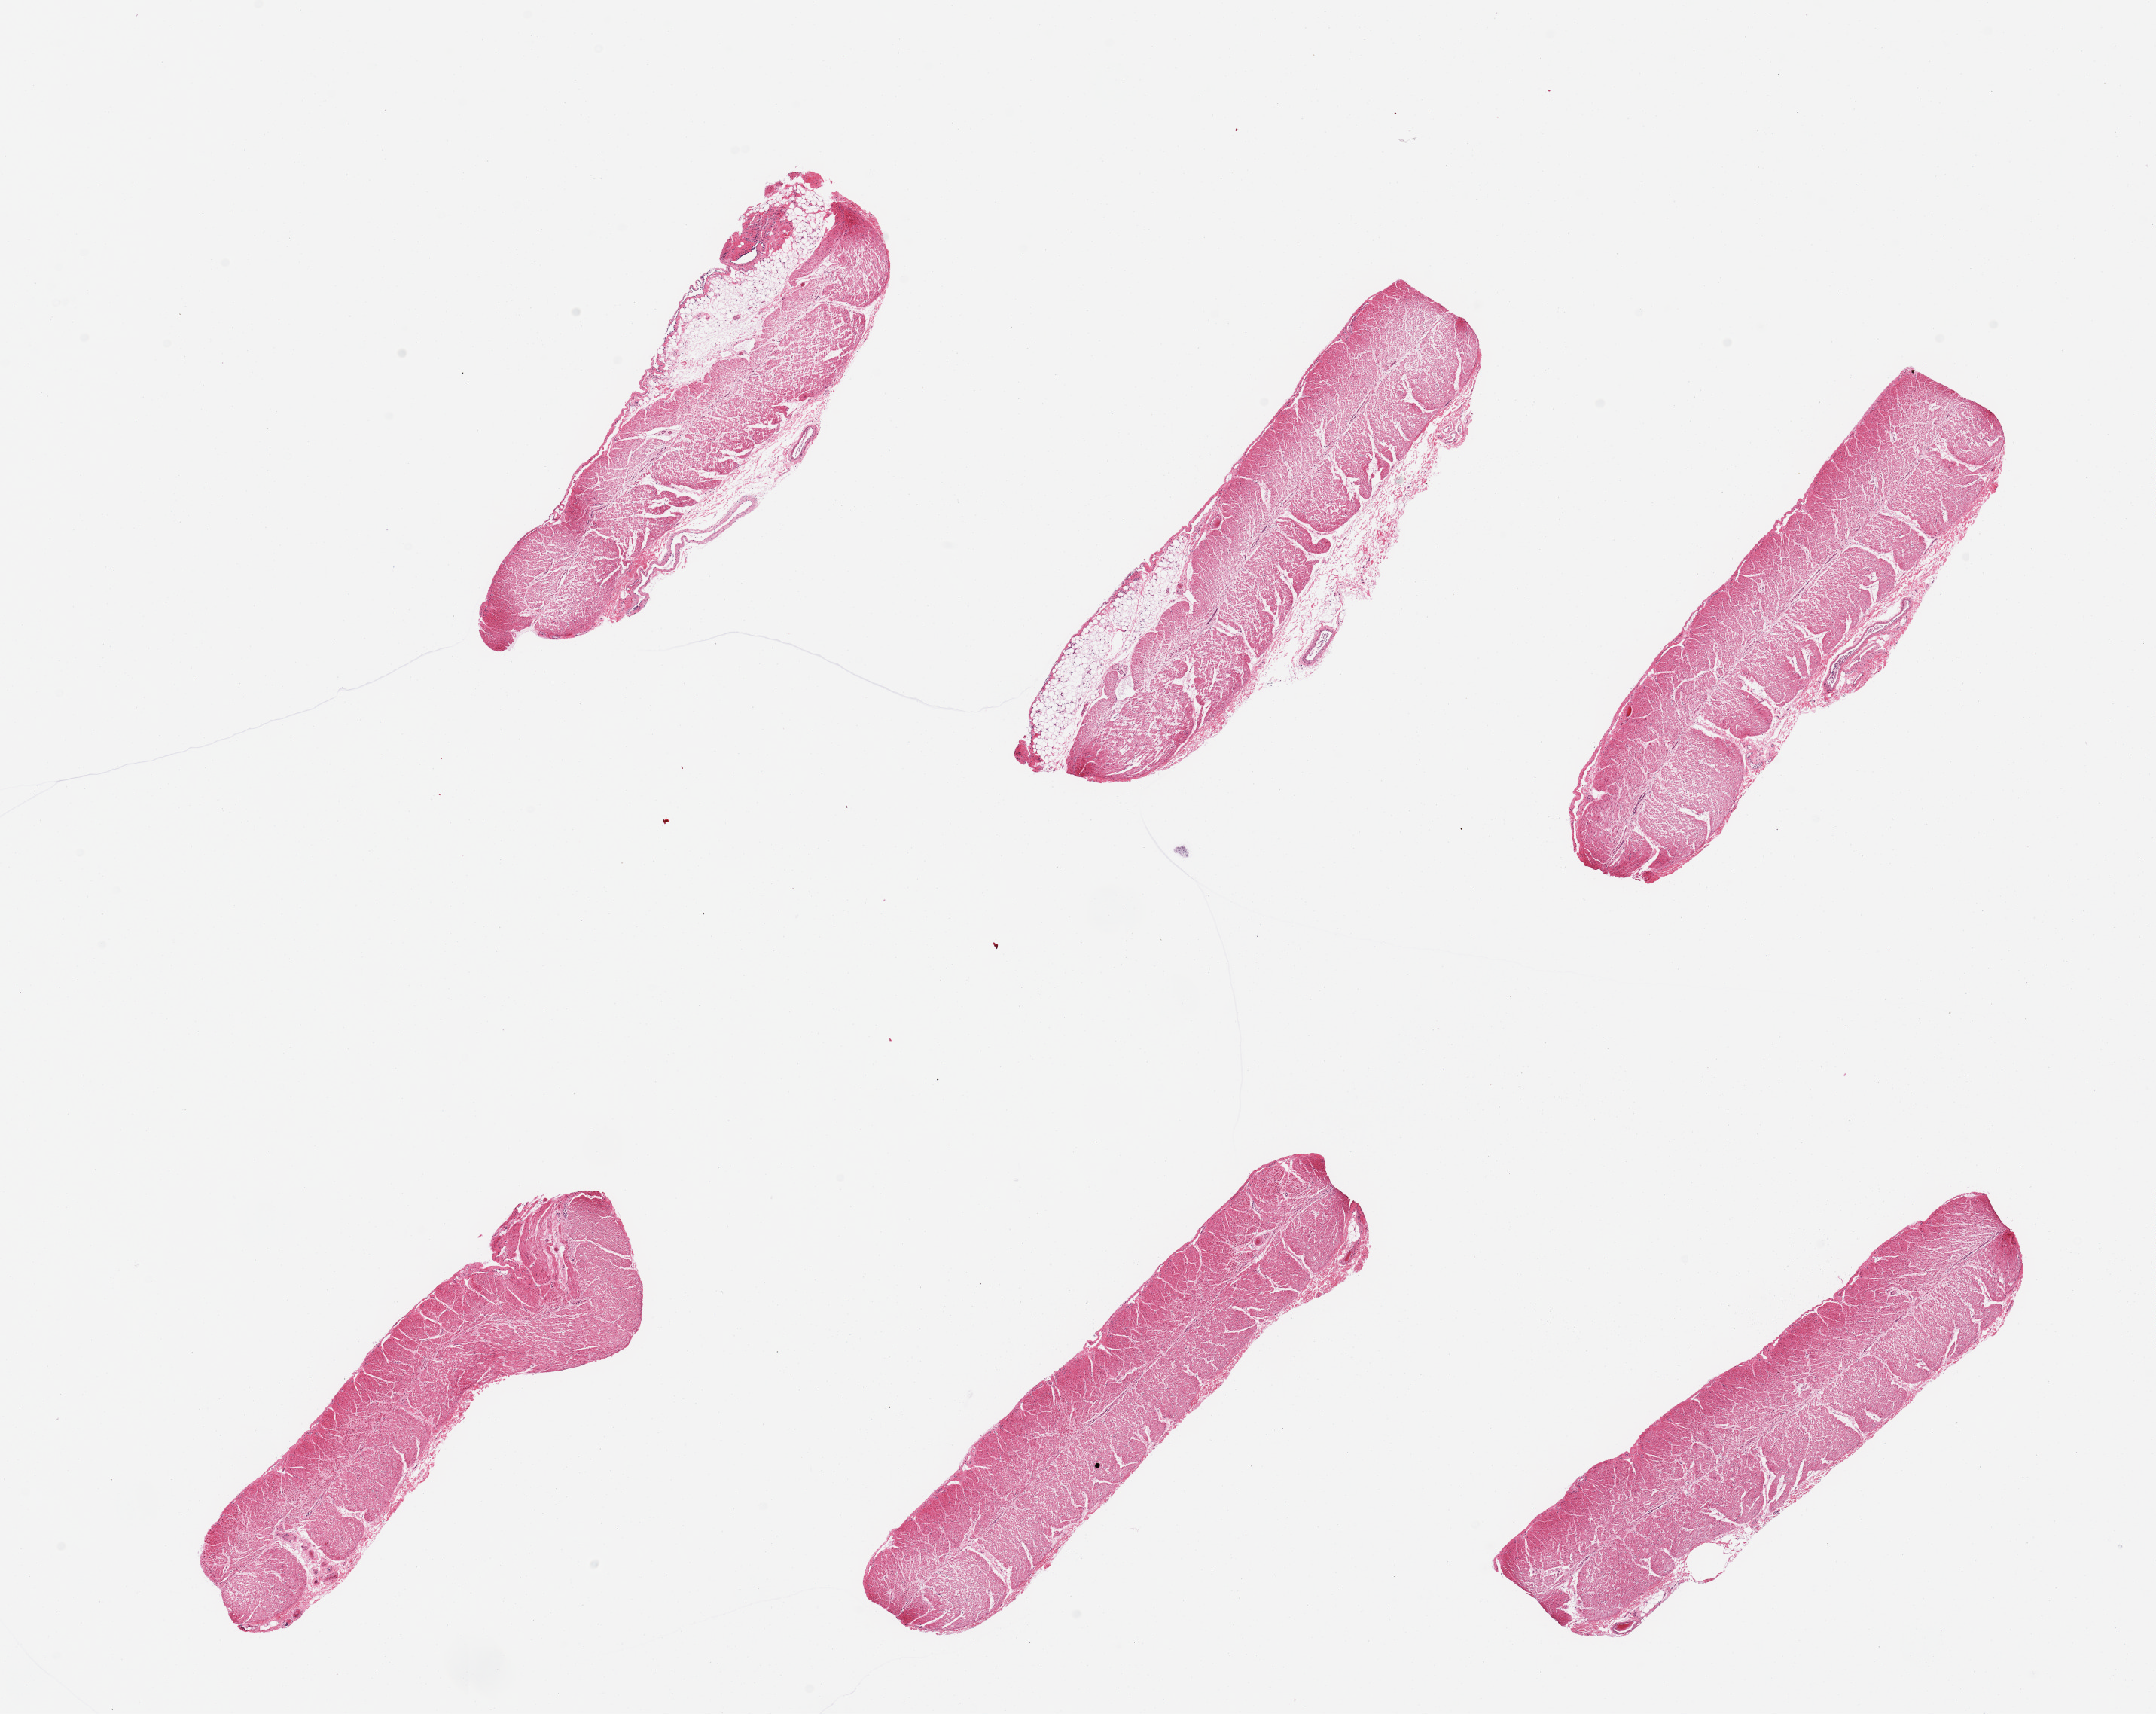
Whole-slide image, hematoxylin and eosin (H&E) stain, shown as a low-resolution overview of the whole scanned area (about 22.6 x 18.0 mm, from a 20x scan); PAXgene-fixed, paraffin-embedded tissue; section of sigmoid colon (target tissue); donor tissue sample. Male donor.
* pathologist's review note for this sample: 6 pieces; target muscularis and thin rim of serosa with fat